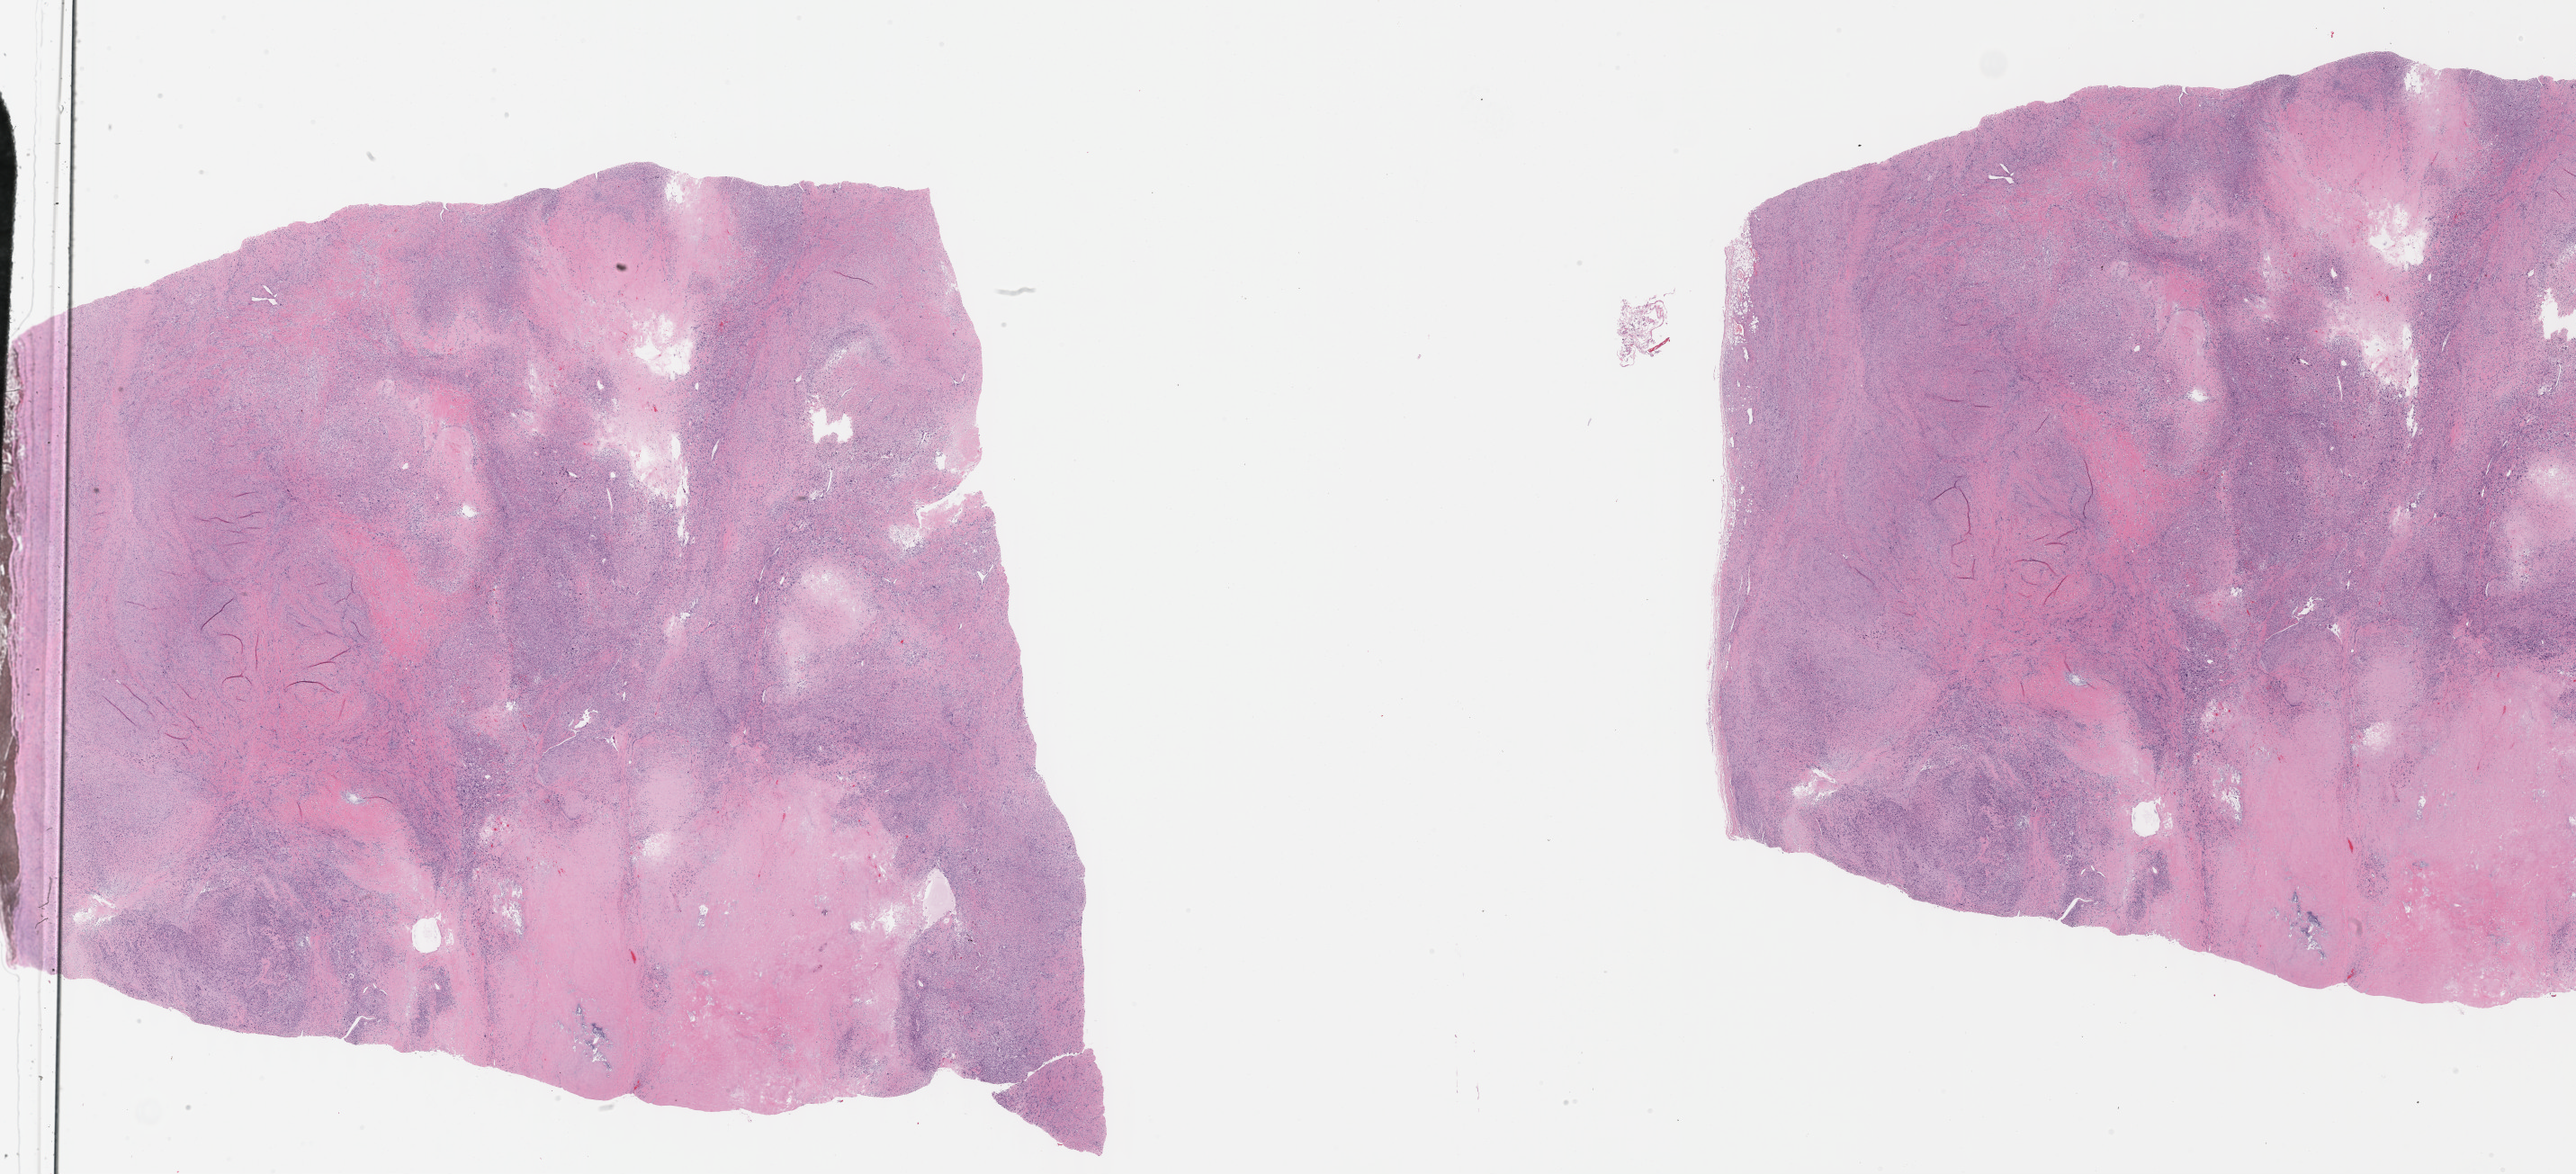
Digitized H&E tissue section (whole slide) — shown as a low-resolution overview of the whole scanned area (about 46.3 x 21.1 mm, slide scanned at 40x); FFPE section; primary tumour sample from the connective, subcutaneous and other soft tissues. Patient: male, age at initial diagnosis 76 years.
Pathologic diagnosis: Malignant fibrous histiocytoma (connective, subcutaneous and other soft tissues of thorax).